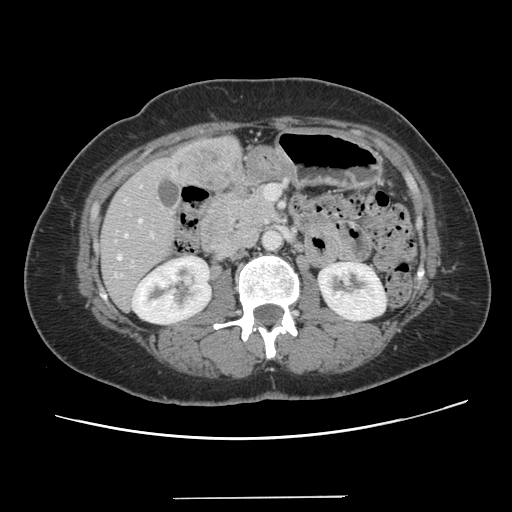
Contrast-enhanced abdominal CT, one axial slice. Position 51 of 141 along the scan axis. Intravenous contrast given. Soft-tissue window (W 400 / L 40 HU). 2.5 mm slice thickness. 512 × 512 image matrix. Female patient, age 53 years. Case-level facts recorded for this patient, not image findings: diagnosis: colorectal cancer liver metastases, imaged before liver resection; multiple liver metastases: no.
Structures marked on this image (outlined manually by an expert reader):
- hepatic veins: bounding box <117,234,126,259> (left, top, right, bottom; pixels)
- liver: <99,137,241,309>
- planned liver remnant (the part of the liver to remain after resection): <99,219,176,309>
- portal vein (with intrahepatic branches): <139,219,152,234>
- liver metastasis: <179,146,235,186>